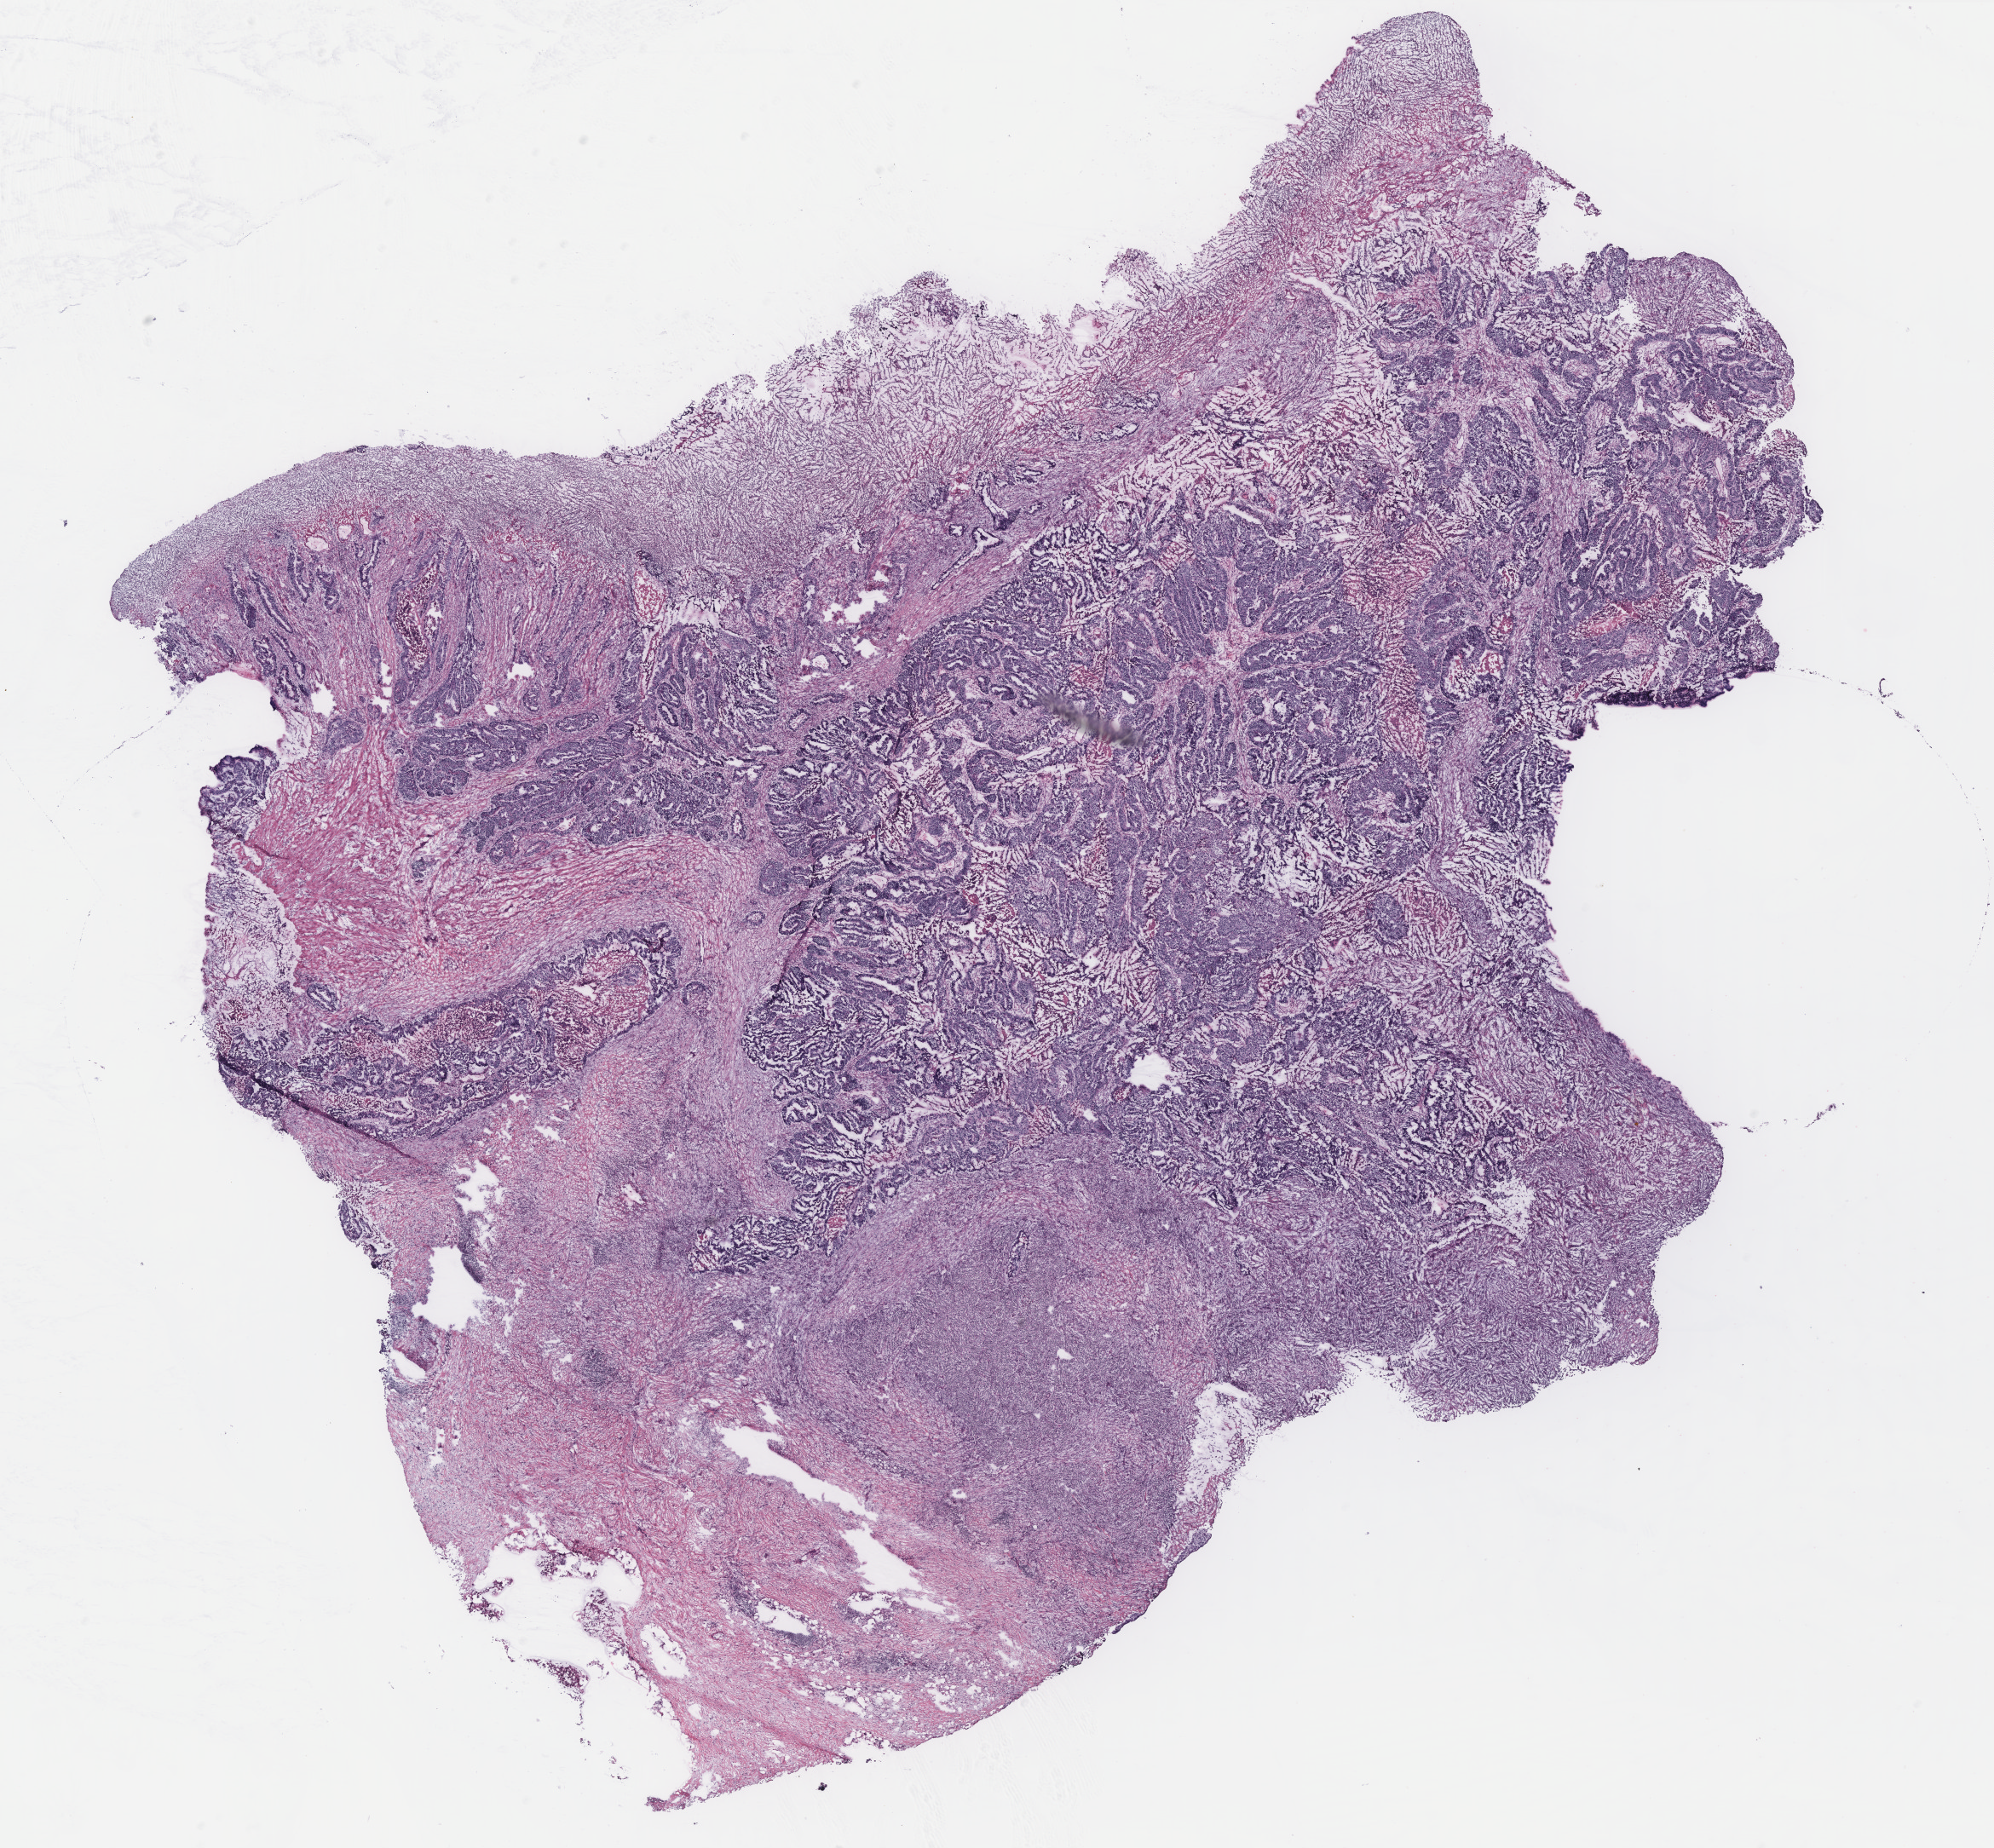
Whole-slide histology image, H&E-stained, low-resolution overview of the scanned area, about 18.7 x 17.4 mm (slide scanned at 40x). Colon, tissue type not recorded.
Patient diagnosis (cohort enrolment): colon cancer (colon).